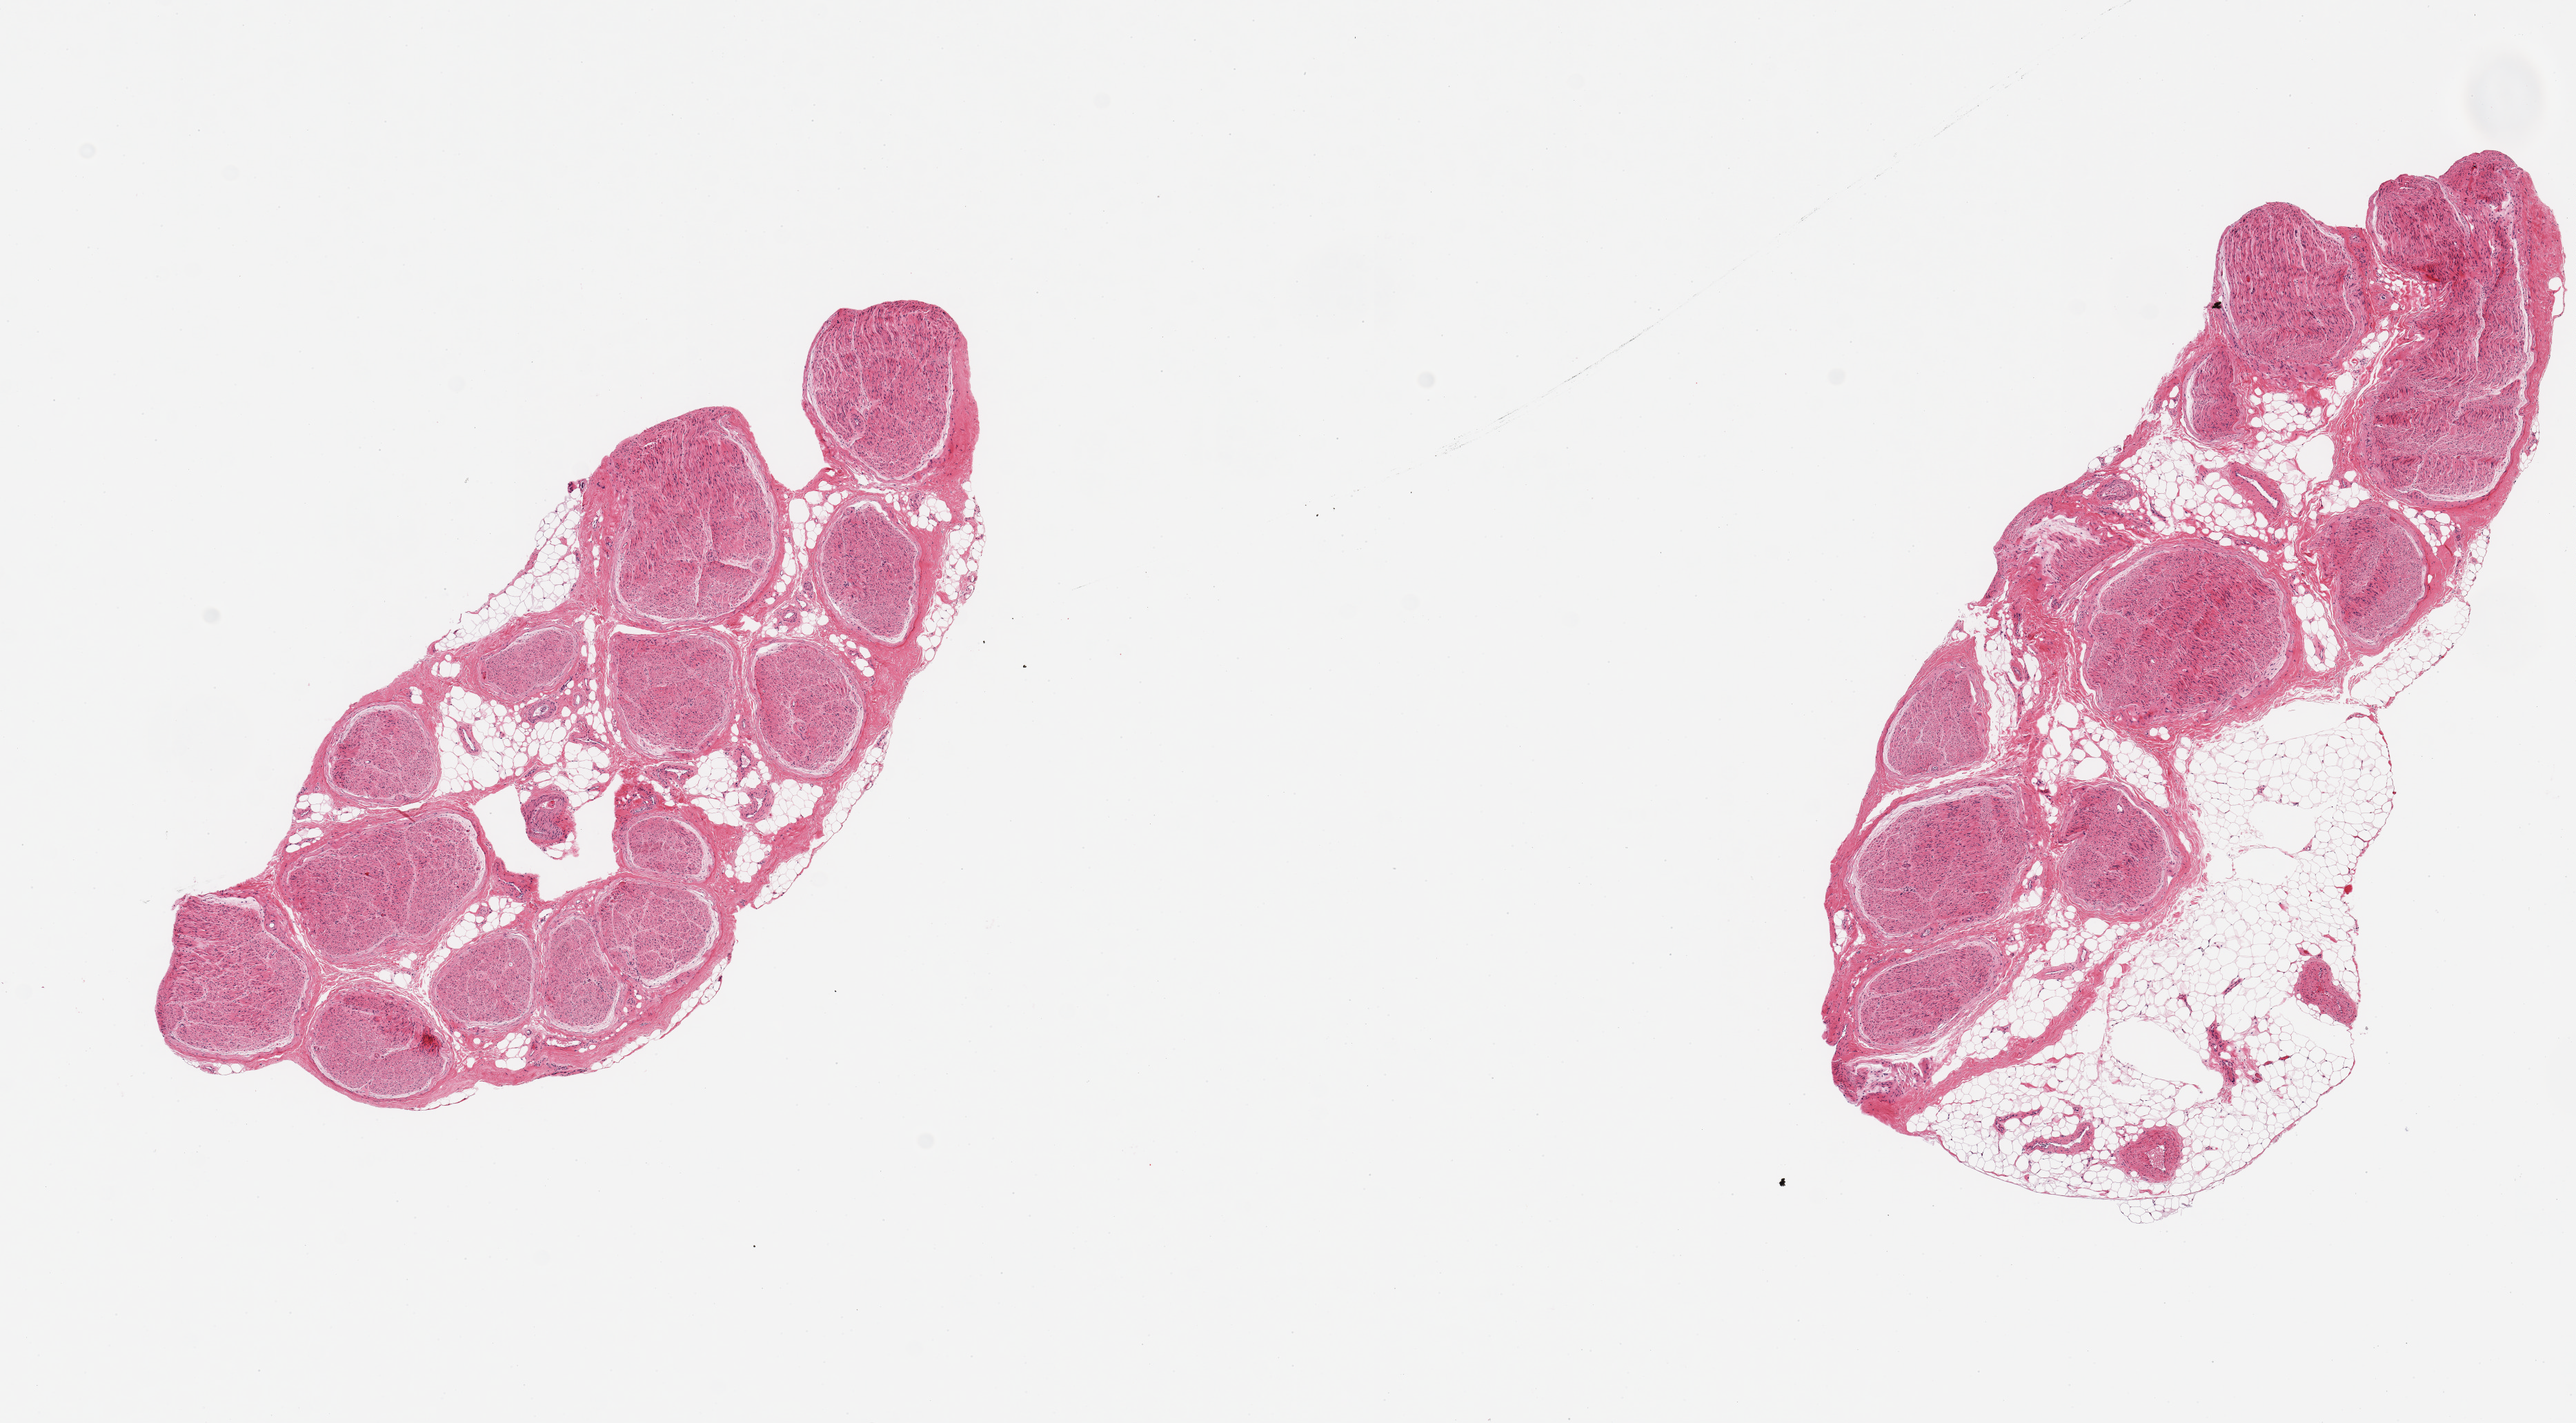
H&E whole-slide image — shown as a low-resolution overview of the whole scanned area (about 14.8 x 8.2 mm). PAXgene-fixed, paraffin-embedded tissue. Sampled site (target tissue): tibial nerve. Tissue donor sample. Donor: female.
* review note (as recorded): 2 pieces, ~1.3mm nubbin of adherent fat